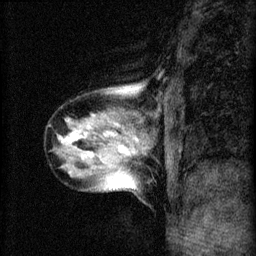
Breast MRI (dynamic contrast-enhanced), one sagittal slice; slice 20 of 60 in the series (ordered by position); 3 images stored at this slice position (order not interpretable as contrast timing); 1.5 T; TE 4.2 ms, TR 8.2 ms; 256 × 256 image matrix, field of view 180 × 180 mm. Female patient, age 40 years.
Annotated regions visible in this slice (semi-automatic segmentation, software-assisted and operator-edited):
- analysis volume of interest (the breast-tissue region the enhancement analysis was run in; not a lesion): bounding box <52,80,164,193> (left, top, right, bottom; pixels)
- tumour enhancement mask (voxels above the 70 % enhancement threshold inside the analysis volume of interest): <67,124,139,157>